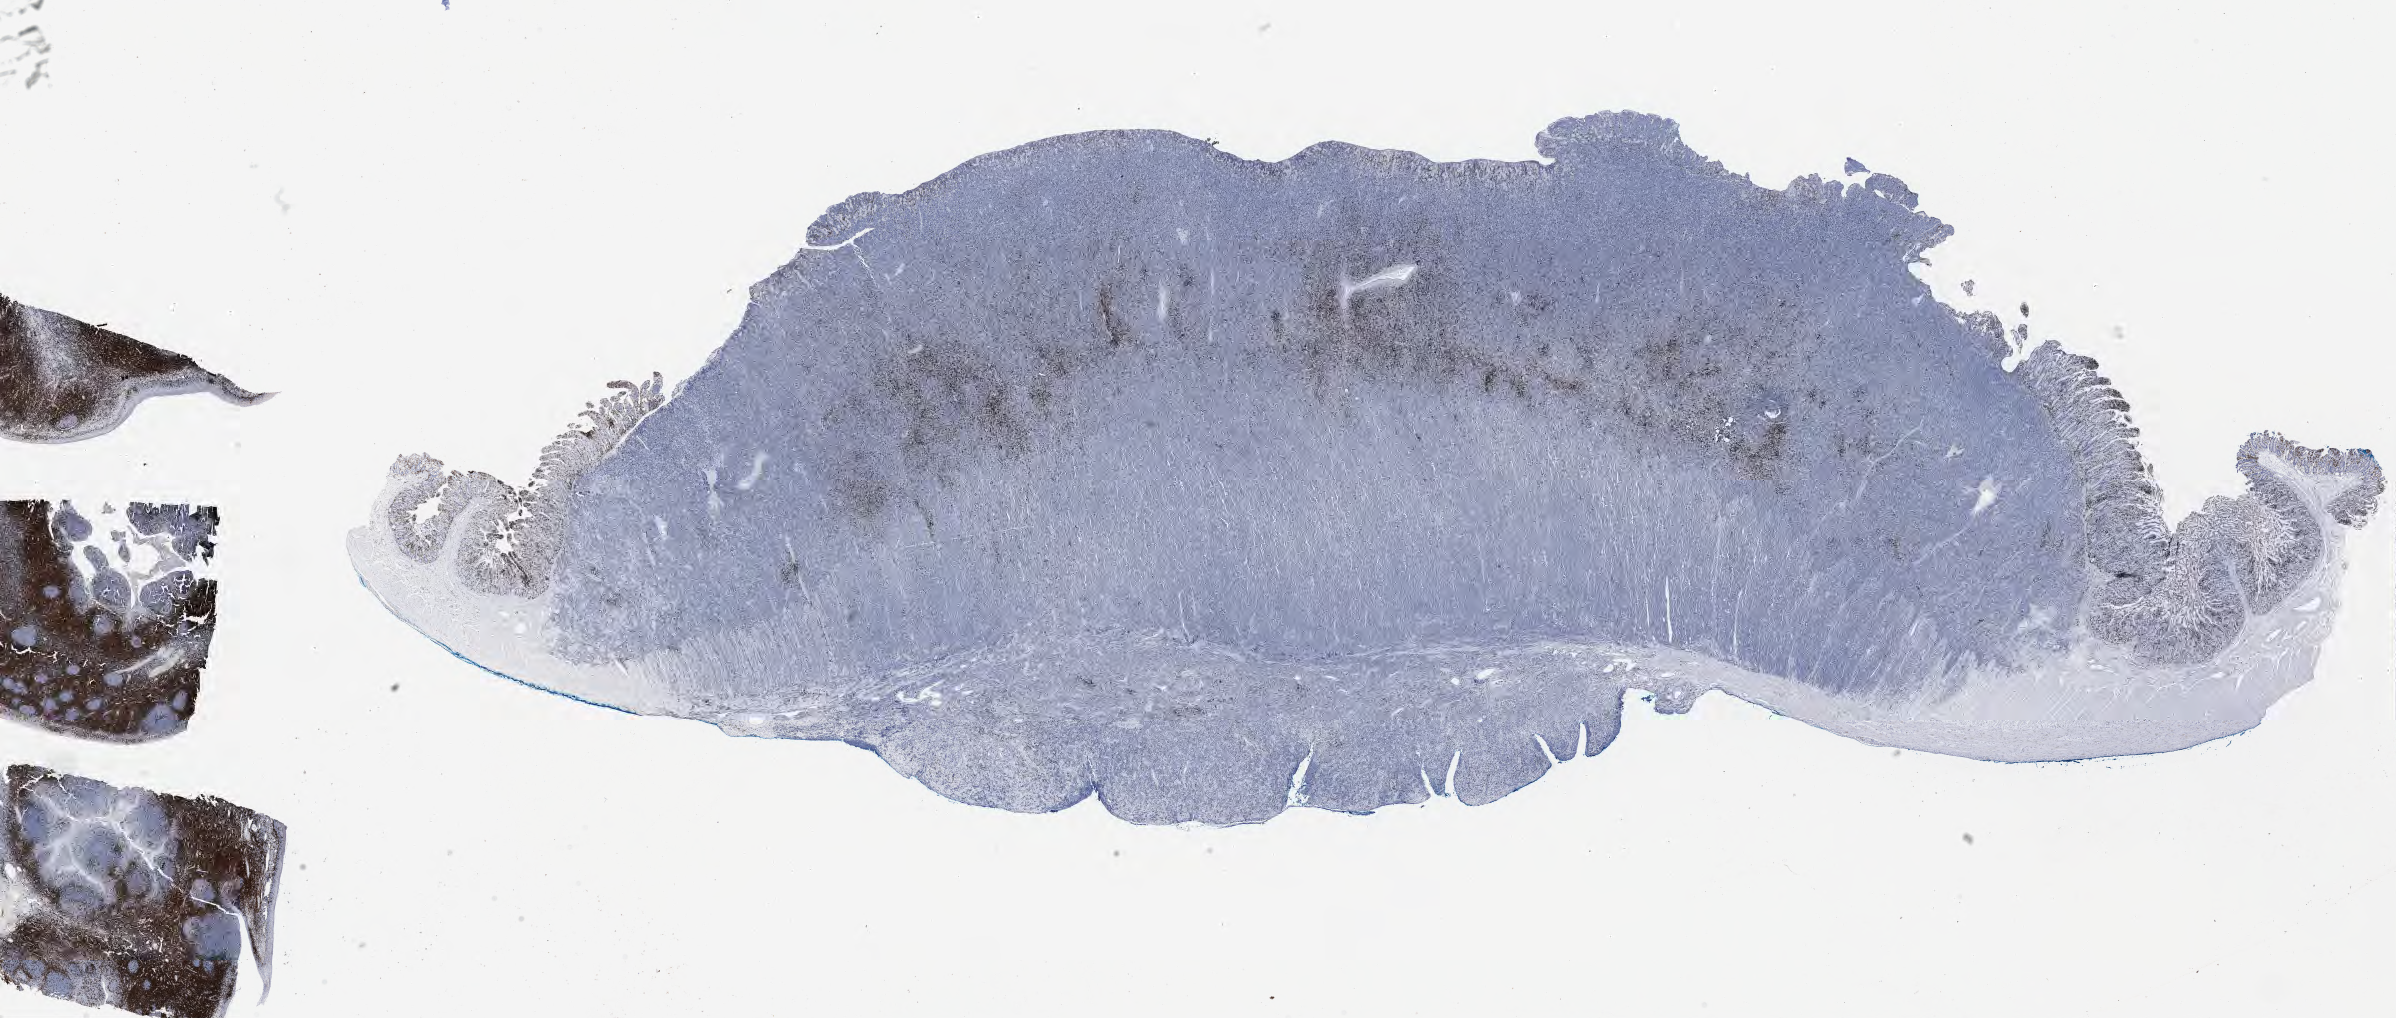
Whole-slide image, immunohistochemical stain for CD3, low-resolution overview of the scanned area, about 38.7 x 16.5 mm, tumor tissue, anatomic site: small intestine. Male patient; age at initial diagnosis 6 years.
Histologic diagnosis: Burkitt lymphoma, NOS.